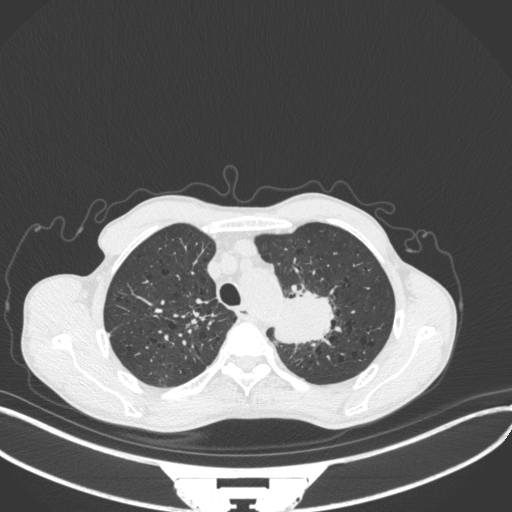
Chest CT, one axial slice. Slice 336 of 394 in the series (ordered by position). Reconstruction kernel B31f. Lung window (W 1500 / L -600 HU). 1 mm slice thickness. 512 × 512 image matrix, field of view 400 × 400 mm. Male patient, age 65 years. Case-level facts recorded for this patient, not image findings: clinical TNM (as recorded): T2b N0 M0; histopathological grade: G2.
Outlined on this slice (rectangle marked by the reading radiologist):
- lung tumour (recorded histology: adenocarcinoma): box from (x=262, y=286) to (x=337, y=348) px